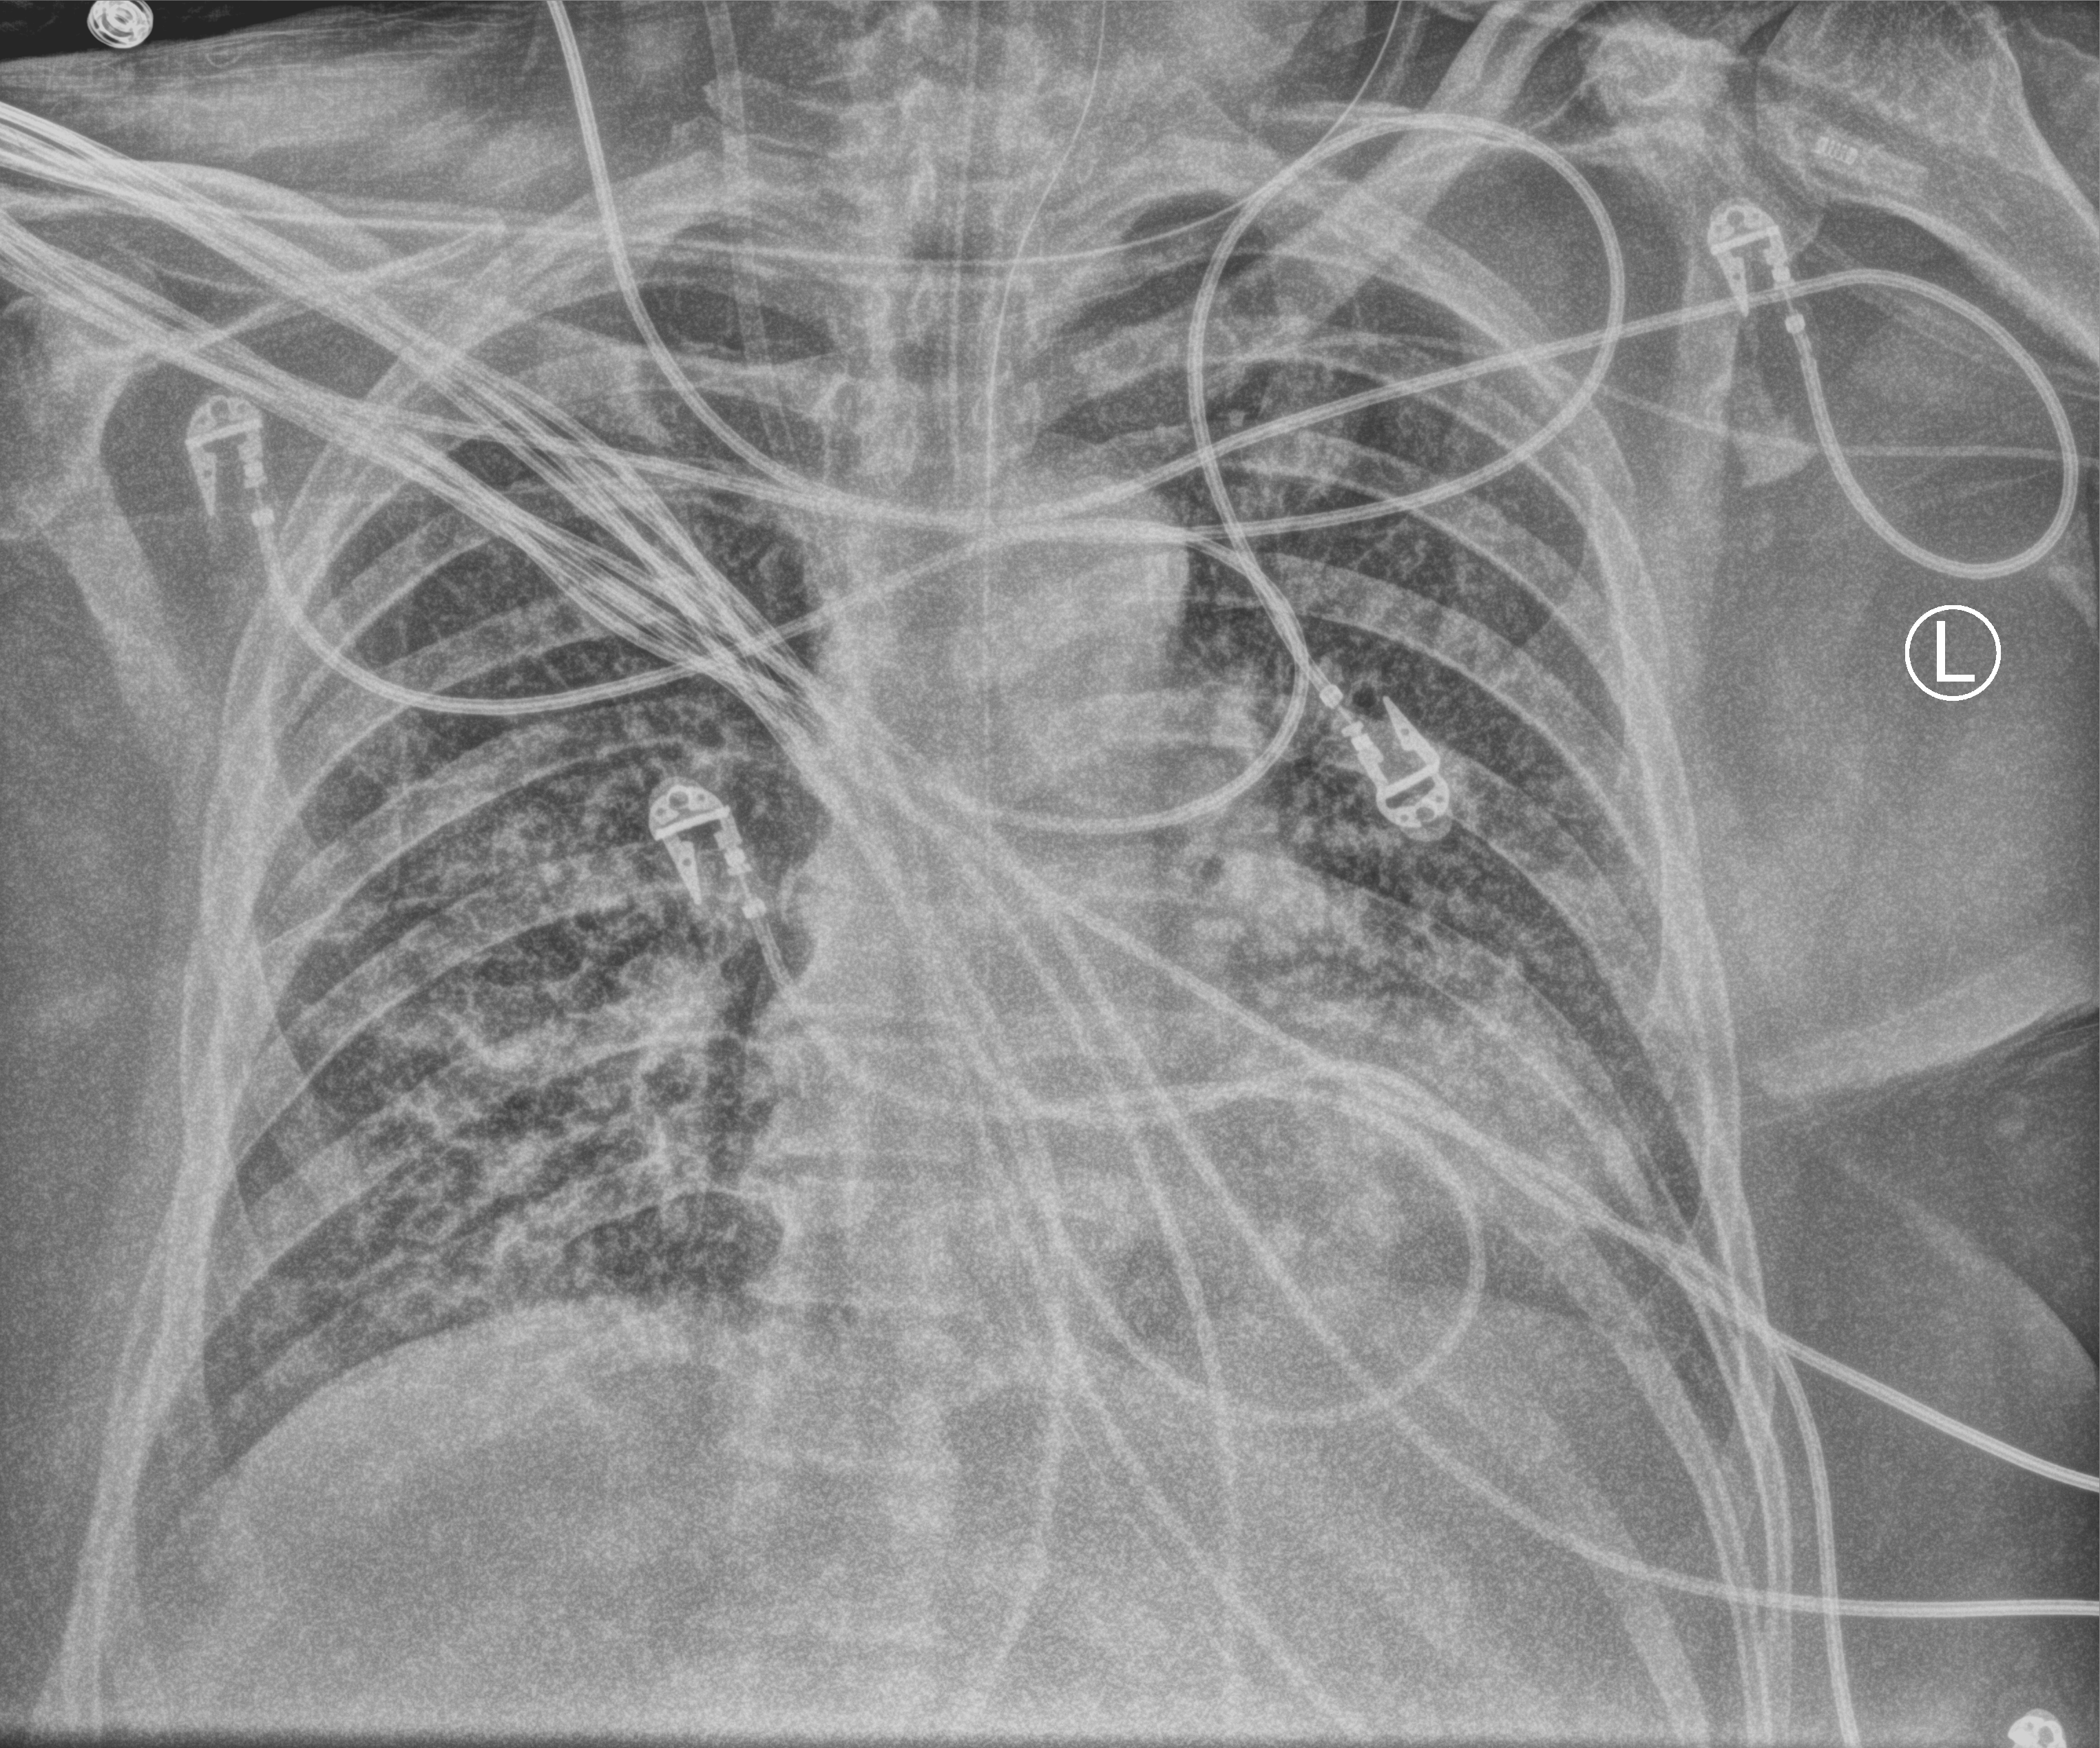
Portable chest radiograph, anteroposterior (AP) projection. Patient hospitalised with COVID-19; male, aged 60–74 years.
Hospital-stay facts (about this admission, not read from this image; timing relative to this image not recorded): COPD (admission record): no; other chronic lung disease (admission record): no; admitted to intensive care during this hospital stay: yes.